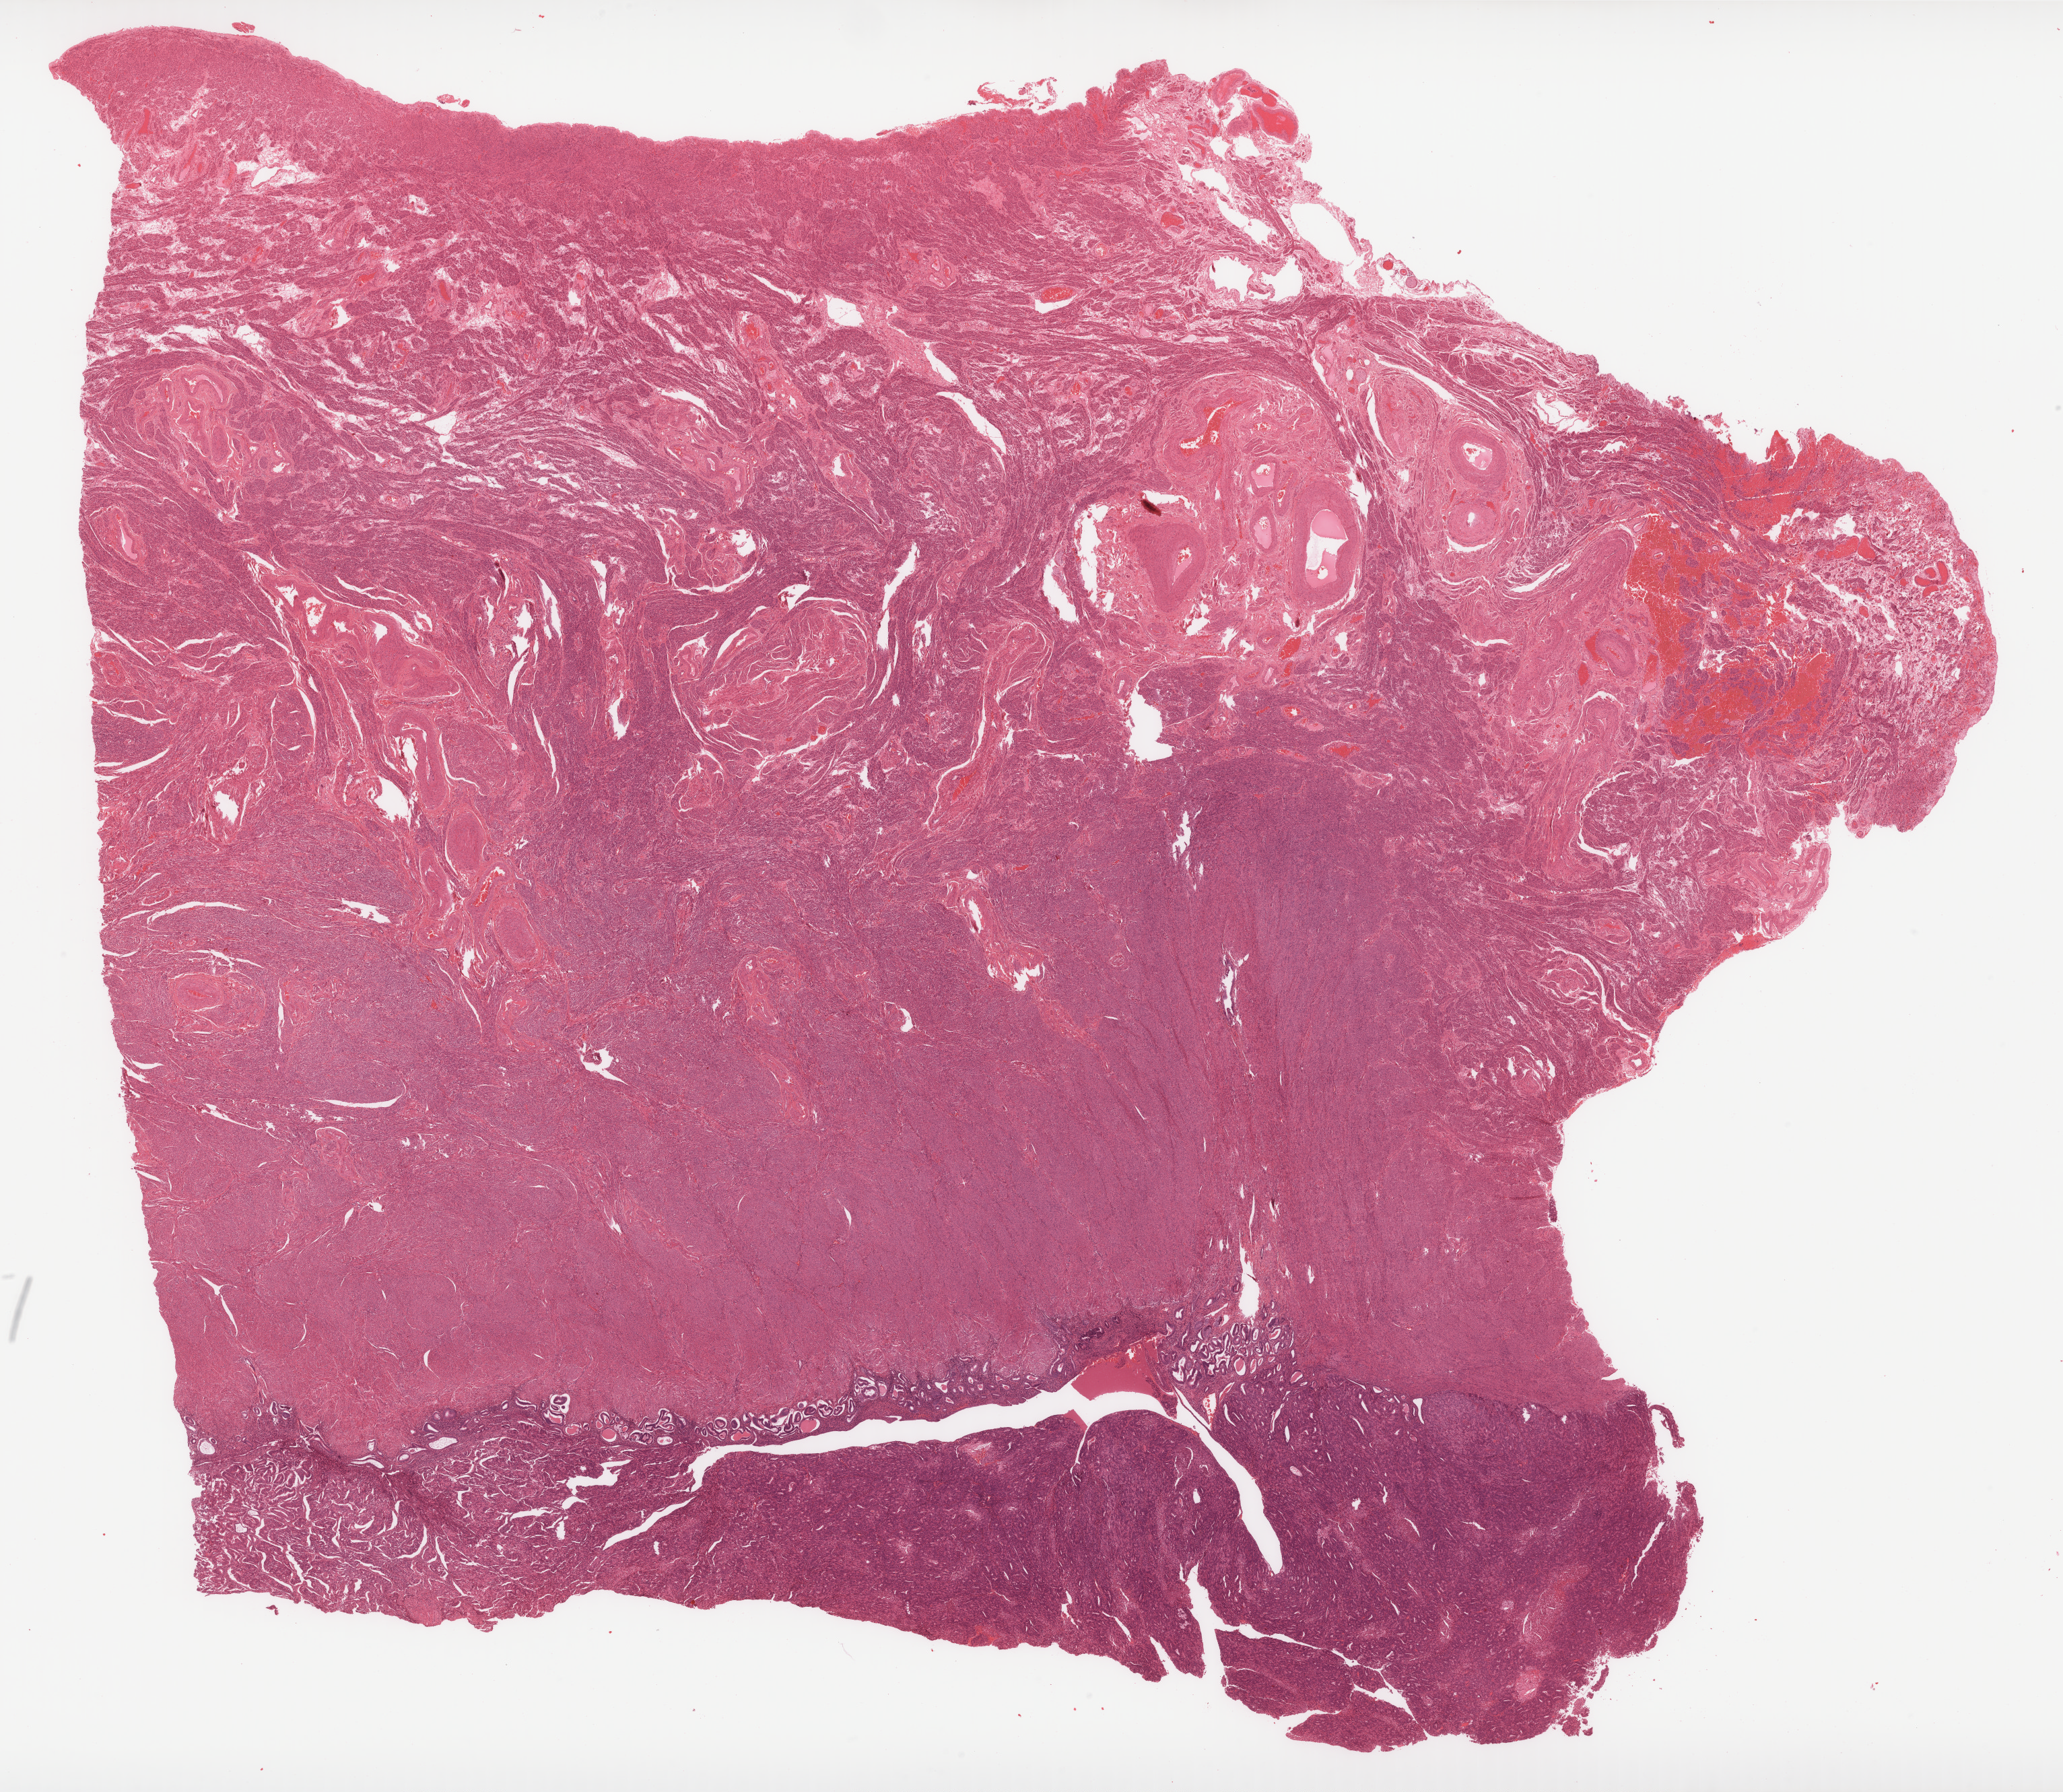
H&E-stained whole-slide image, low-resolution overview of the scanned area, about 24.7 x 21.4 mm (acquisition: 40x scan), formalin-fixed paraffin-embedded (FFPE) diagnostic section, uterus, primary tumour sample. Female patient; age at initial diagnosis 68 years. Histologic grade: G3 (poorly differentiated).
FIGO stage: IA. Histologic diagnosis: Endometrioid adenocarcinoma, NOS (endometrium).